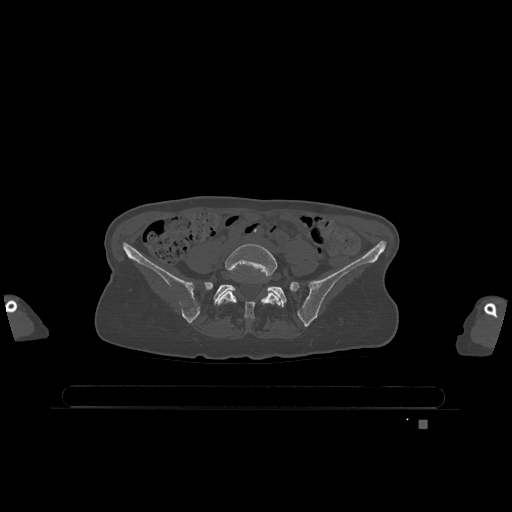
CT including the spine, one axial slice. Position 222 of 1317 along the scan axis. Bone window (W 1800 / L 400 HU). 512 × 512 image matrix, field of view 500 × 500 mm. Female patient, age 74 years. Case-level facts recorded for this patient, not image findings: primary cancer: lung.
Structures marked on this image (semi-automatically segmented with operator editing):
- L5 vertebra: bounding box [x1, y1, x2, y2] px = [217, 244, 281, 319]